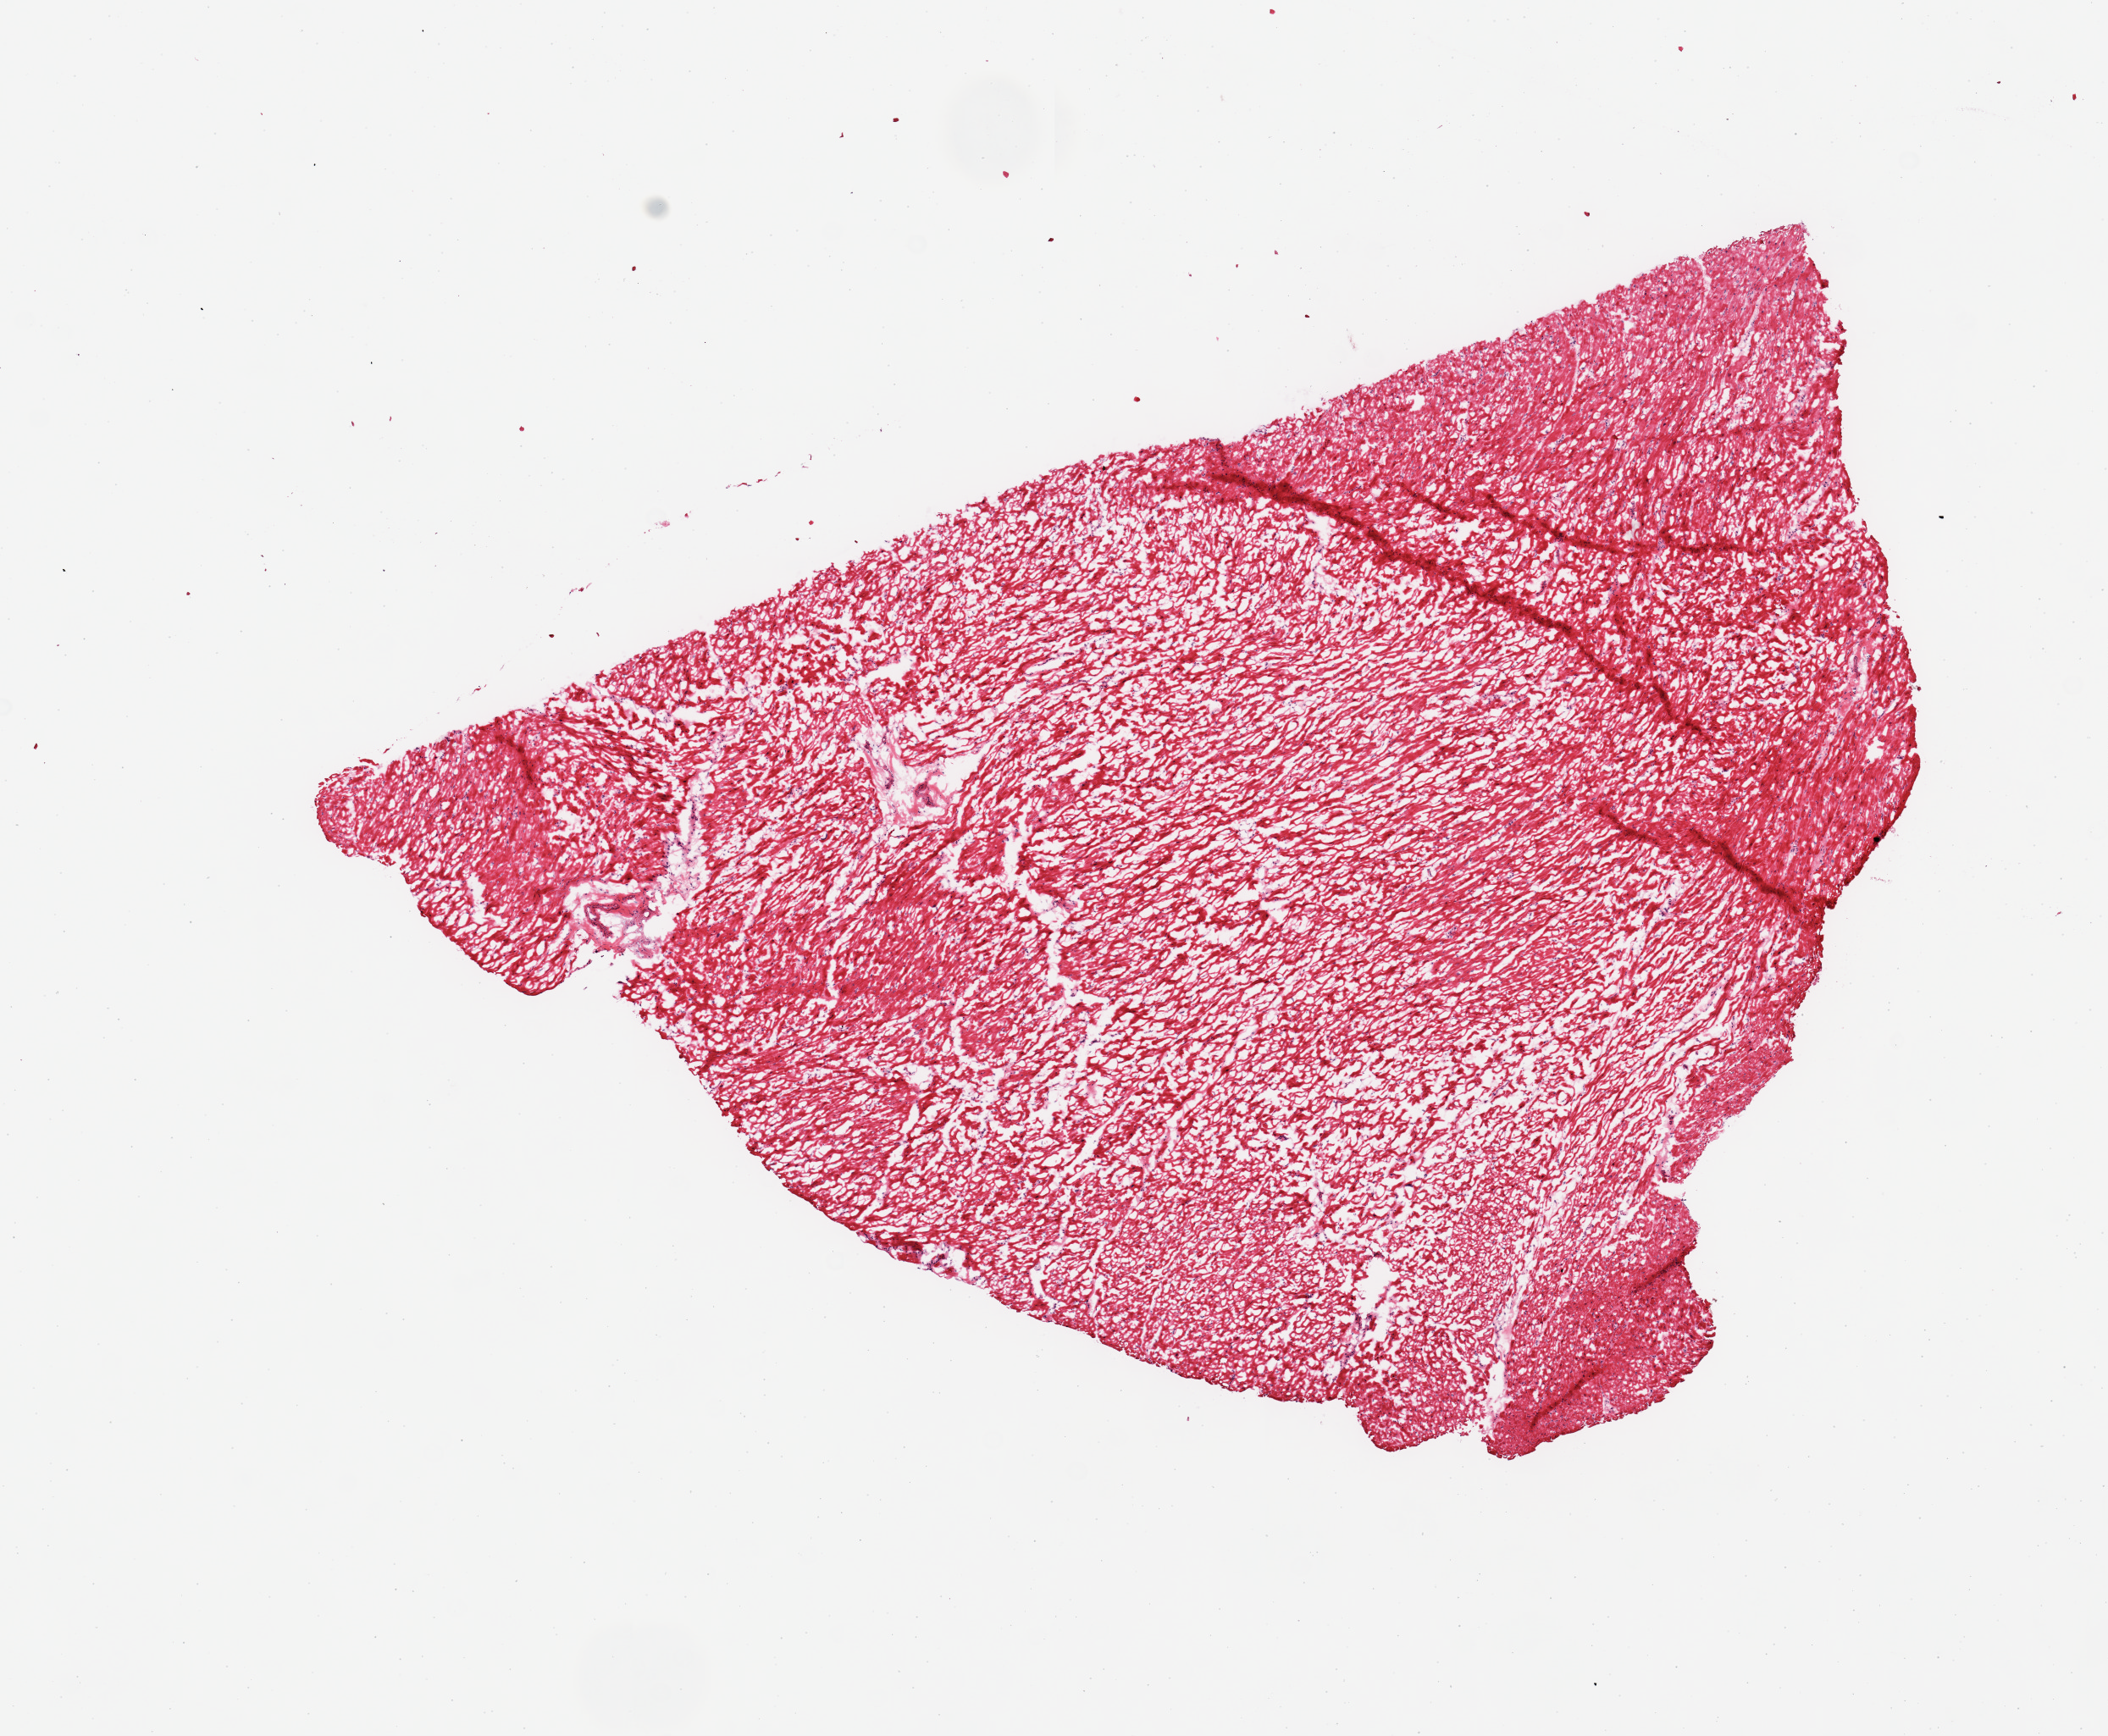
Whole-slide image, haematoxylin and eosin stain, brightfield — whole scanned area (about 9.8 x 8.1 mm, from a 20x scan) shown as a low-resolution overview, frozen section, target tissue: heart, tissue donor sample. Male donor.
* pathologist's review note for this sample: 1 piece